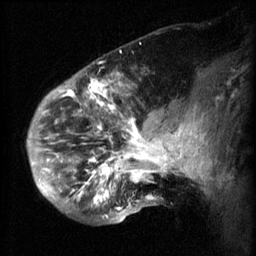
Breast MRI (dynamic contrast-enhanced), one sagittal slice. Position 19 of 60 along the scan axis. 3 images stored at this slice position (order not interpretable as contrast timing). 1.5 T. TE 4.2 ms, TR 8.2 ms. 2.3 mm slice thickness. 256 × 256 image matrix, field of view 200 × 200 mm. Patient: female, 50 years.
Structures marked on this image (semi-automatic segmentation, software-assisted and operator-edited):
- analysis volume of interest (the breast-tissue region the enhancement analysis was run in; not a lesion): bounding box (x1, y1, x2, y2) in pixels: (50, 64, 169, 217)
- tumour enhancement mask (voxels above the 70 % enhancement threshold inside the analysis volume of interest): (50, 74, 169, 217)